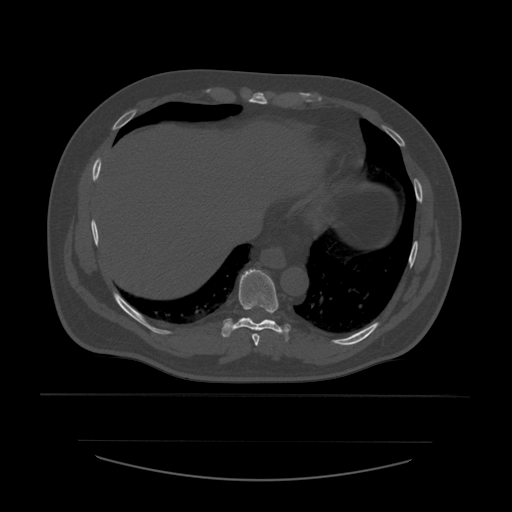
CT including the spine, one axial slice; slice 318 of 532 in the series (ordered by position); reconstruction kernel STANDARD; 120 kVp; bone window (W 1800 / L 400 HU); 1.25 mm slice thickness; 512 × 512 image matrix, field of view 441 × 441 mm. Patient age 44 years. Case-level facts recorded for this patient, not image findings: primary cancer: soft tissue sarcoma.
Outlined on this slice (semi-automatically segmented with operator editing):
- T8 vertebra: bounding box (x1, y1, x2, y2) in pixels: (252, 334, 260, 346)
- T9 vertebra: (221, 270, 291, 342)